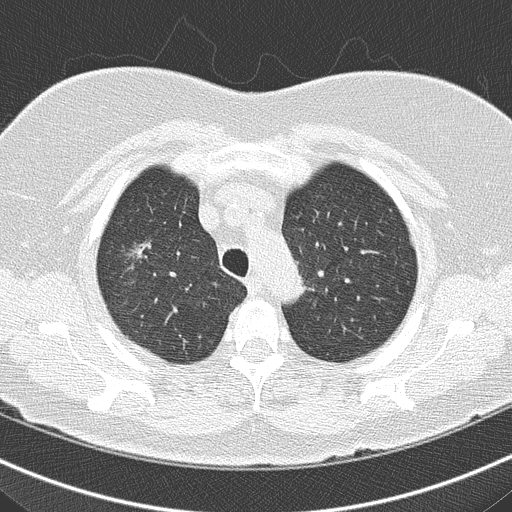
Chest CT (low-dose screening protocol), one axial image. Third annual screen. Lung window (W 1500 / L -600 HU). 2 mm slice thickness. Lung (sharp) reconstruction kernel (B50f). Slice 138 of 161 in the series. 512 × 512 image matrix. Female participant, aged 74 years at enrolment. Former smoker at enrolment.
- Expert reader's lesion annotation, bounding box [x1, y1, x2, y2] px = [110, 231, 177, 295].
- The screening reader recorded 5 non-calcified nodules or masses ≥4 mm on this exam; which of them this box marks is not recorded.
- Later outcome: lung cancer diagnosed 117 days after this screen — bronchiolo-alveolar carcinoma, non-mucinous, right upper lobe, well differentiated (G1), stage IA (AJCC 6th edition), 14 mm at pathology.